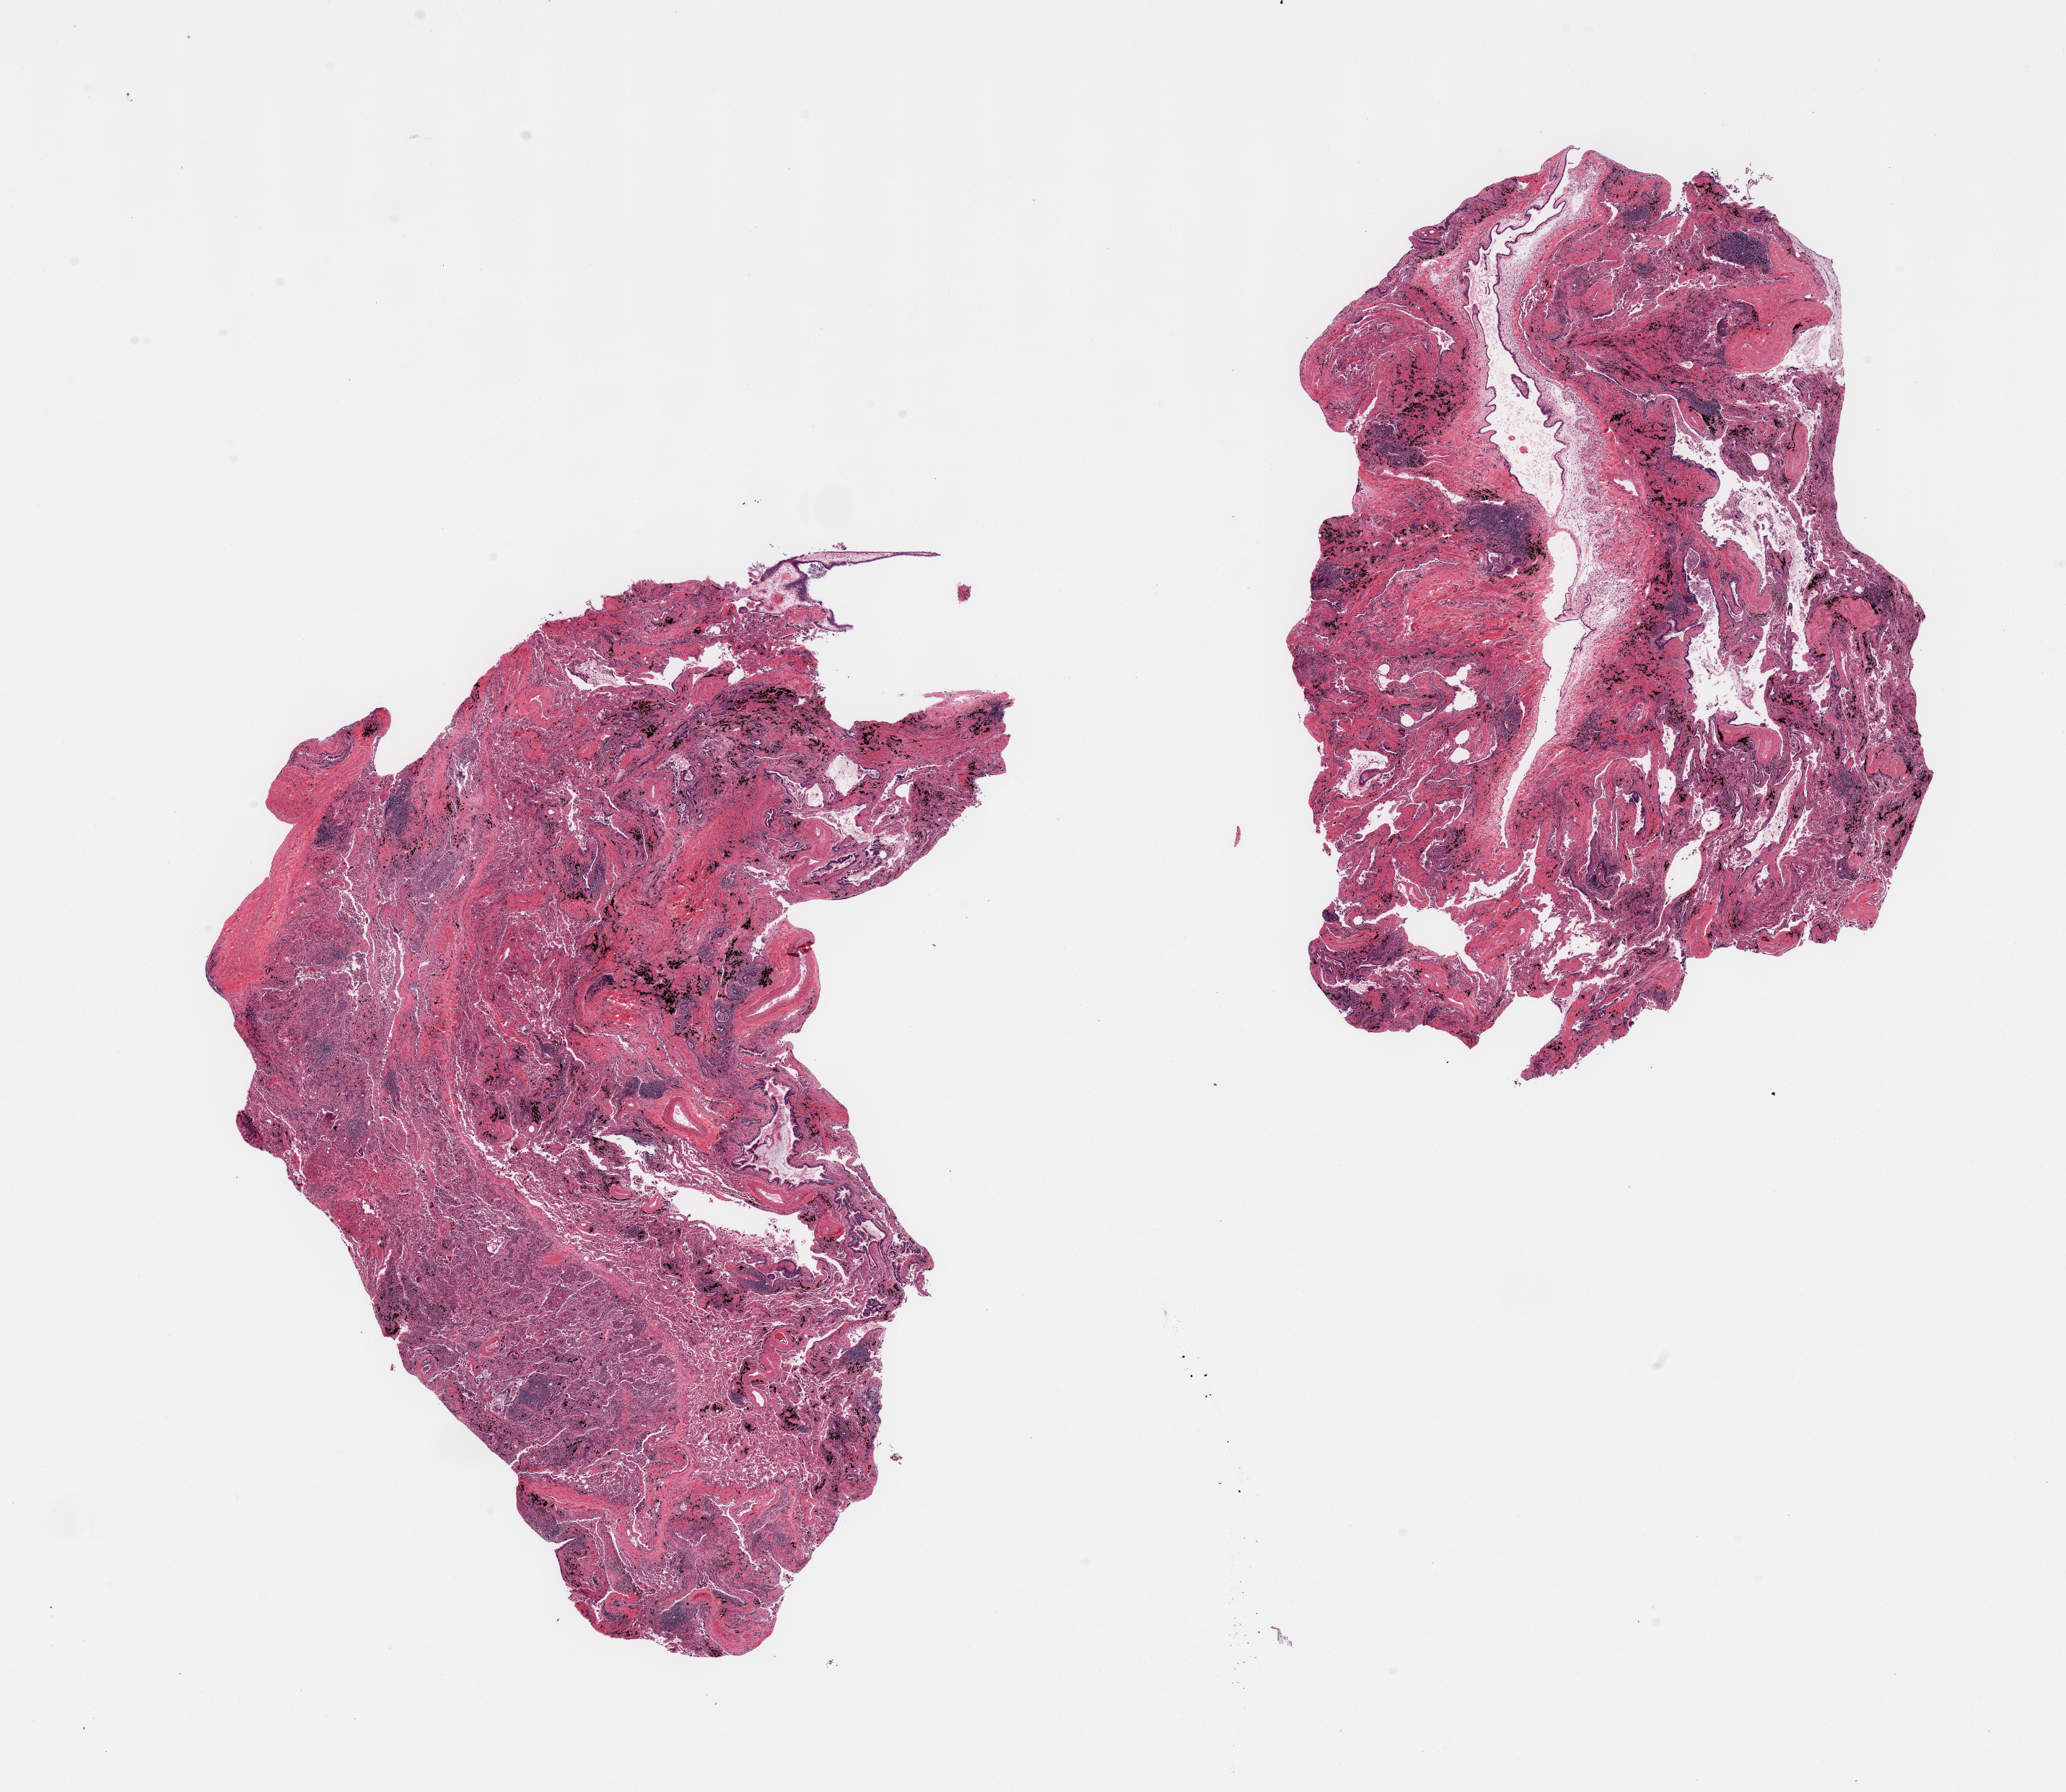
Hematoxylin and eosin (H&E) whole-slide image, shown as a low-resolution overview of the whole scanned area (about 22.6 x 19.6 mm, slide scanned at 20x). PAXgene-fixed, paraffin-embedded tissue. Section of lung (target tissue). Tissue donor sample. Female donor.
* pathologist's review note for this sample: 2 pieces; collapsed alveolar spaces; severe interstitial fibrosis and bronchitis; prominent peribronchial lymphoid tissue aggregates; thick-walled pulmonary vessels; bronchiectasis; bronchi and bronchioles contain desquamated lining cells, inflammatory cells and mucus; prominent anthracosis